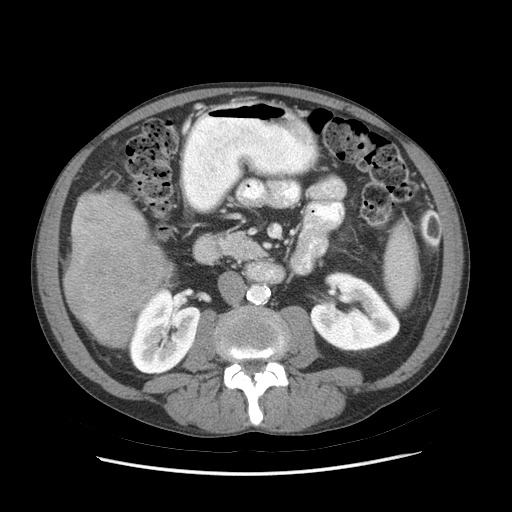
Contrast-enhanced abdominal CT (liver protocol), one axial slice; position 21 of 89 along the scan axis; soft-tissue window (W 400 / L 40 HU); 2.5 mm slice thickness; 512 × 512 image matrix, field of view 380 × 380 mm. Case-level facts recorded for this patient, not image findings: diagnosis: hepatocellular carcinoma (patient treated with transarterial chemoembolisation; whether this scan precedes or follows treatment is not stated here); TNM stage (as recorded): Stage-IIIB; Child-Pugh class: A; tumour differentiation: moderately differentiated; tumour nodularity: multinodular.
Outlined on this slice (semi-automatic segmentation, software-assisted and operator-edited):
- liver parenchyma outside the tumour (the mass and vessels are separate outlines, so this box may not span the whole liver): bounding box [x1, y1, x2, y2] px = [64, 190, 172, 324]
- mass: [64, 227, 169, 349]